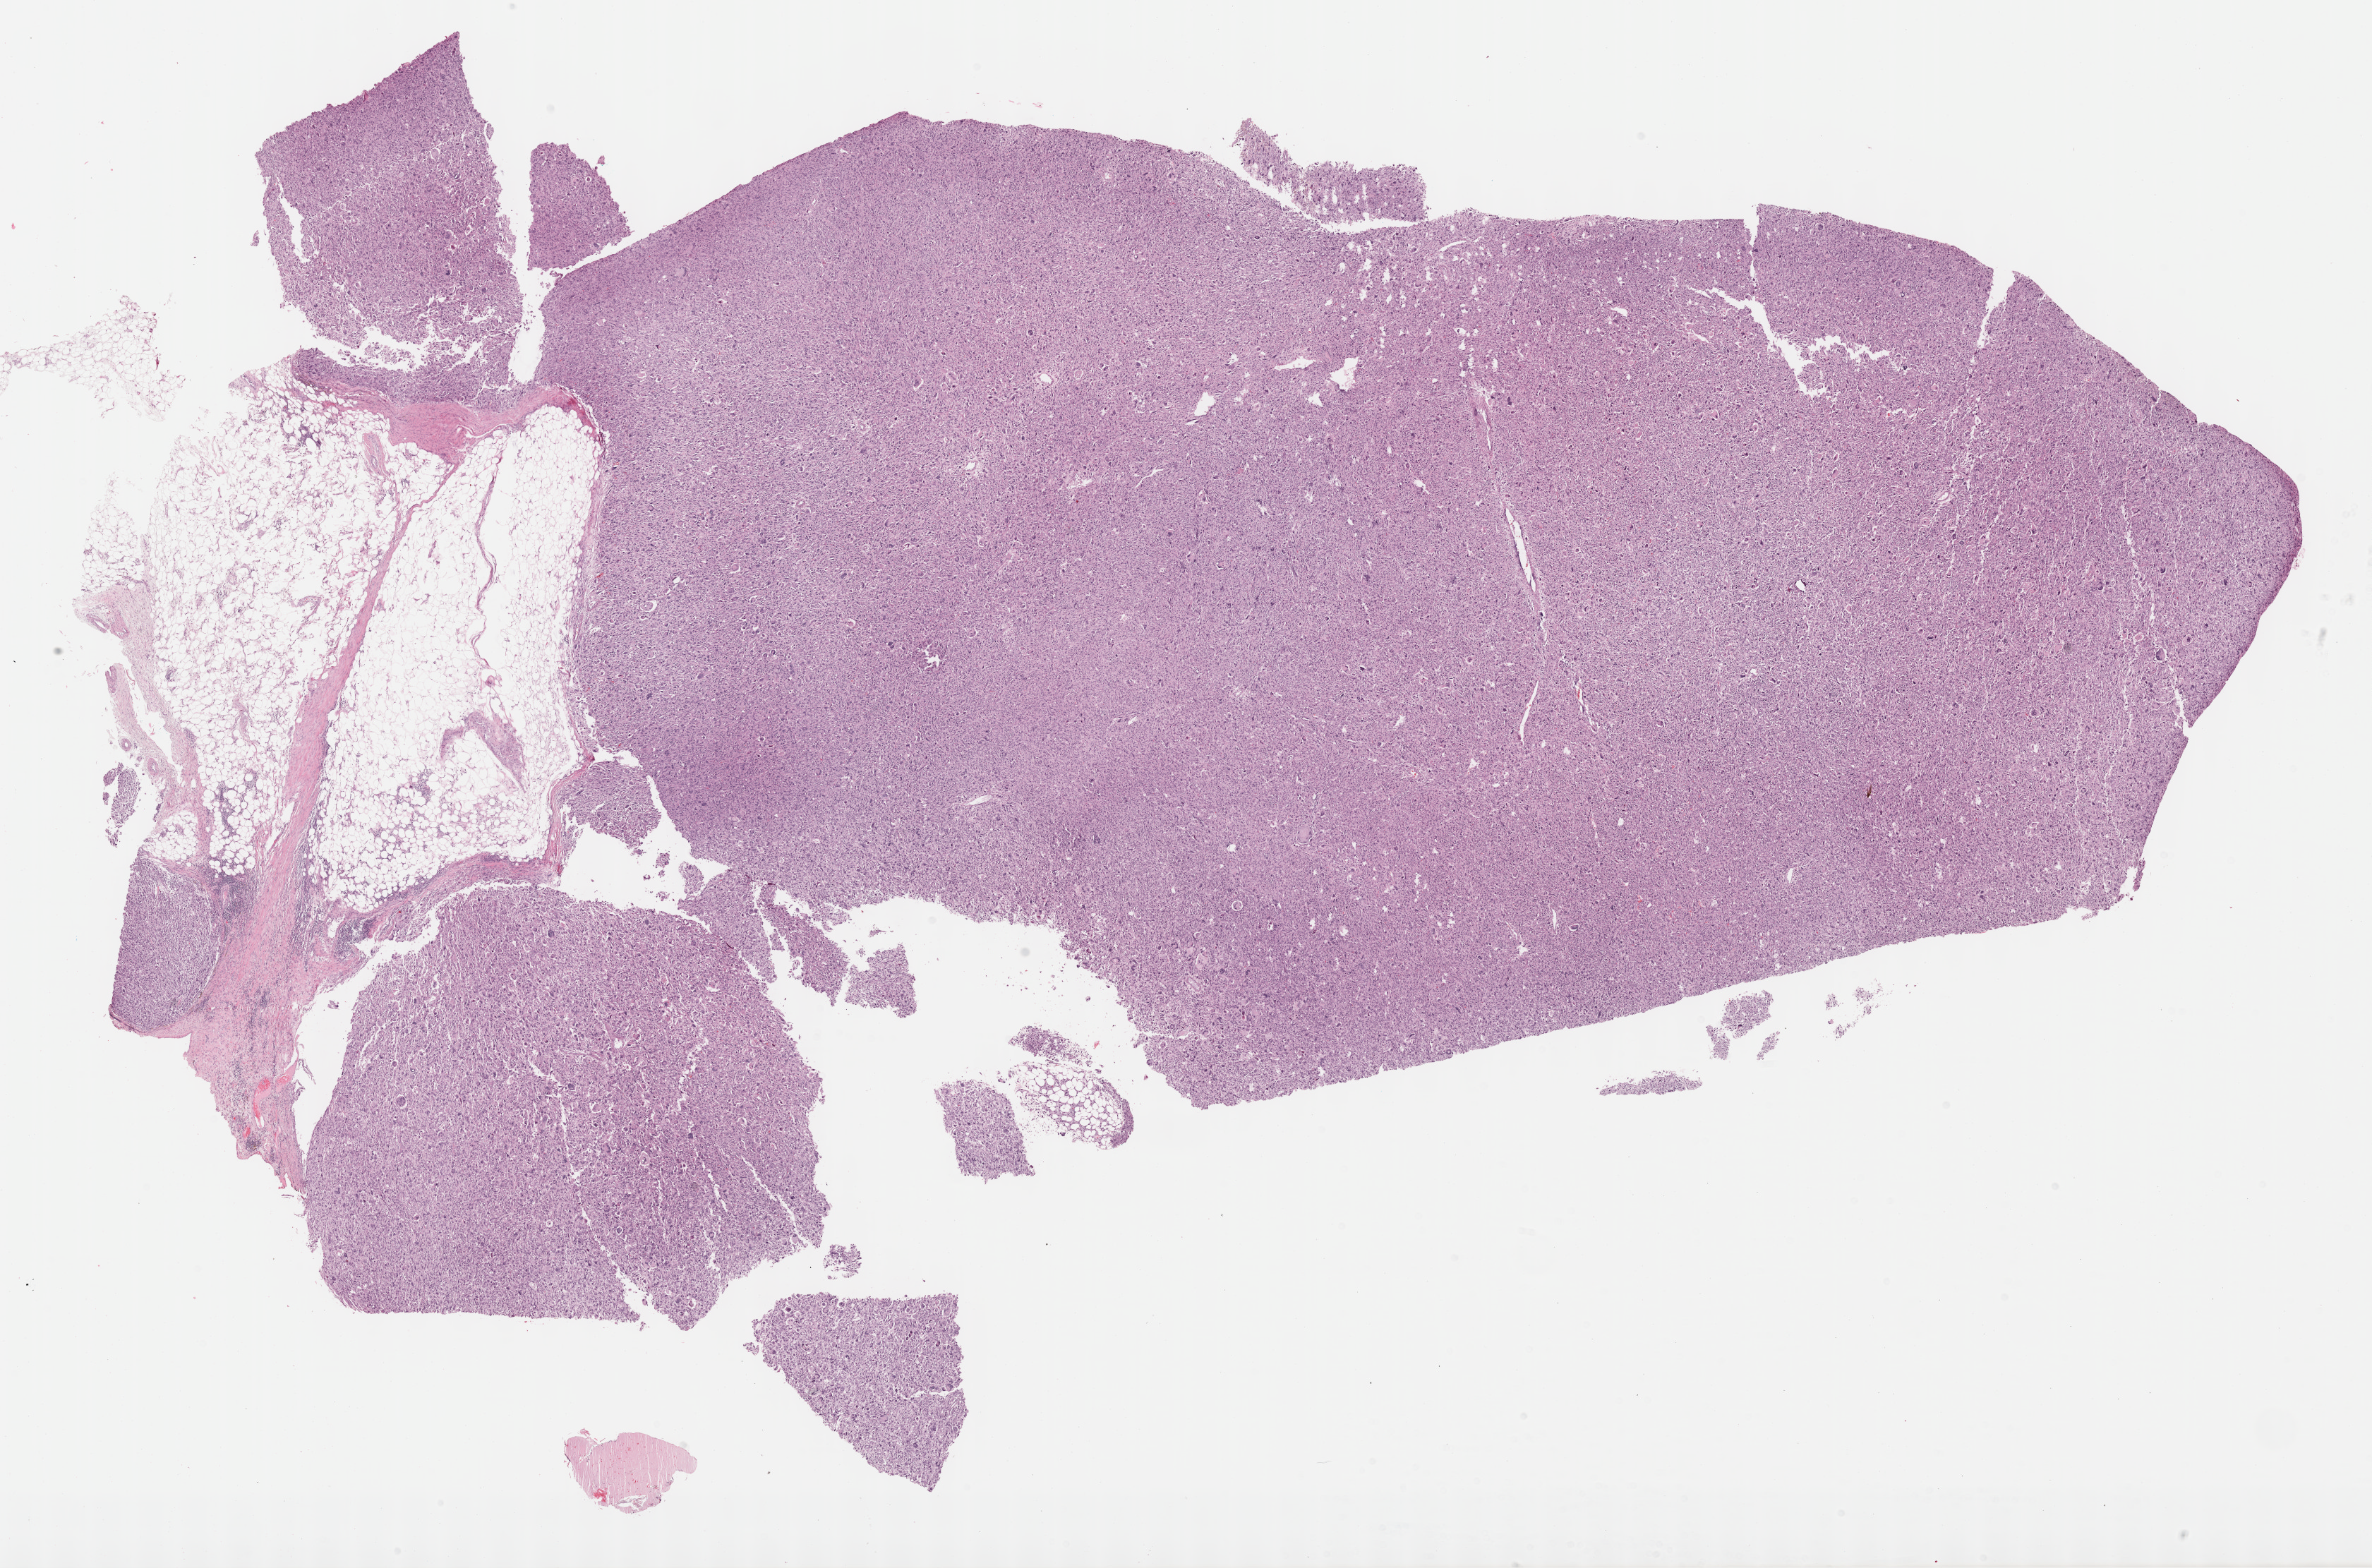
Digitized H&E-stained tissue section (whole slide) — whole scanned area (about 27.2 x 18.0 mm) shown as a low-resolution overview. Formalin-fixed paraffin-embedded (FFPE) diagnostic section. Primary tumour sample from the connective, subcutaneous and other soft tissues. Female, age 65 years at initial diagnosis.
• pathologic diagnosis: Malignant fibrous histiocytoma (connective, subcutaneous and other soft tissues of lower limb and hip)